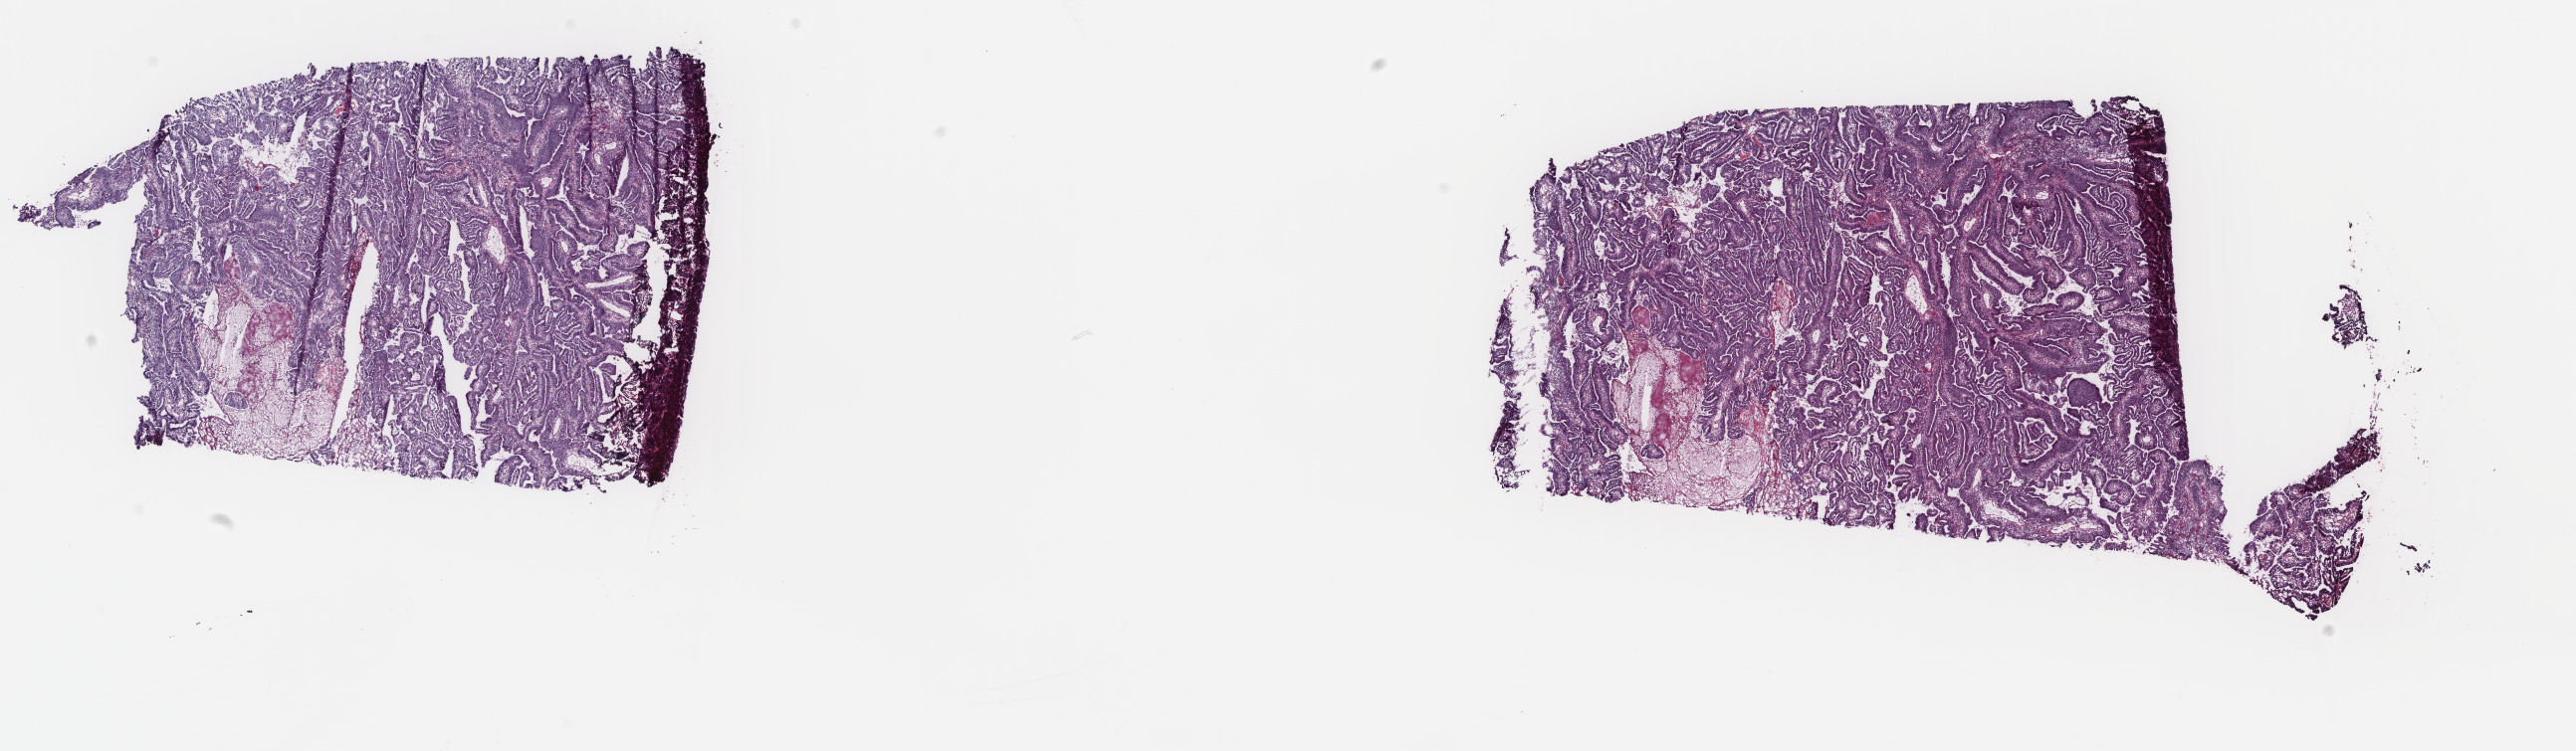
Whole-slide histology image, H&E-stained, whole scanned area (about 20.5 x 6.0 mm, from a 40x scan) shown as a low-resolution overview, frozen section, cervix, primary tumour sample. Female patient; age at initial diagnosis 25 years. Histologic grade: GX (grade cannot be assessed). Pathologist review of this section (percent, as recorded): tumour cells 80%, tumour nuclei 80%, normal cells 0%, stromal cells 10%, necrosis 10%. Infiltration values recorded for this section: lymphocyte infiltration 40%, monocyte infiltration 10%, neutrophil infiltration 30%.
FIGO stage: IB1. Lymph nodes positive (case pathology): 0 of 12 examined. Diagnosis: Adenocarcinoma, NOS (cervix uteri).